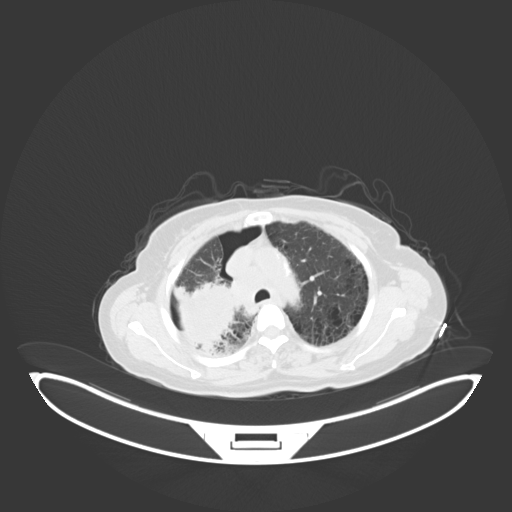
Chest CT, one axial slice; position 45 of 69 along the scan axis; reconstruction kernel B30f; 120 kVp; lung window (W 1500 / L -600 HU); 3 mm slice thickness; 512 × 512 image matrix, field of view 500 × 500 mm. Female patient, age 64 years. From the clinical record (not read from this slice): clinical TNM (as recorded): T3 N3 M0.
Annotated regions visible in this slice (rectangle marked by the reading radiologist):
- lung tumour (recorded histology: squamous cell carcinoma): bounding box [x1, y1, x2, y2] px = [167, 277, 238, 353]